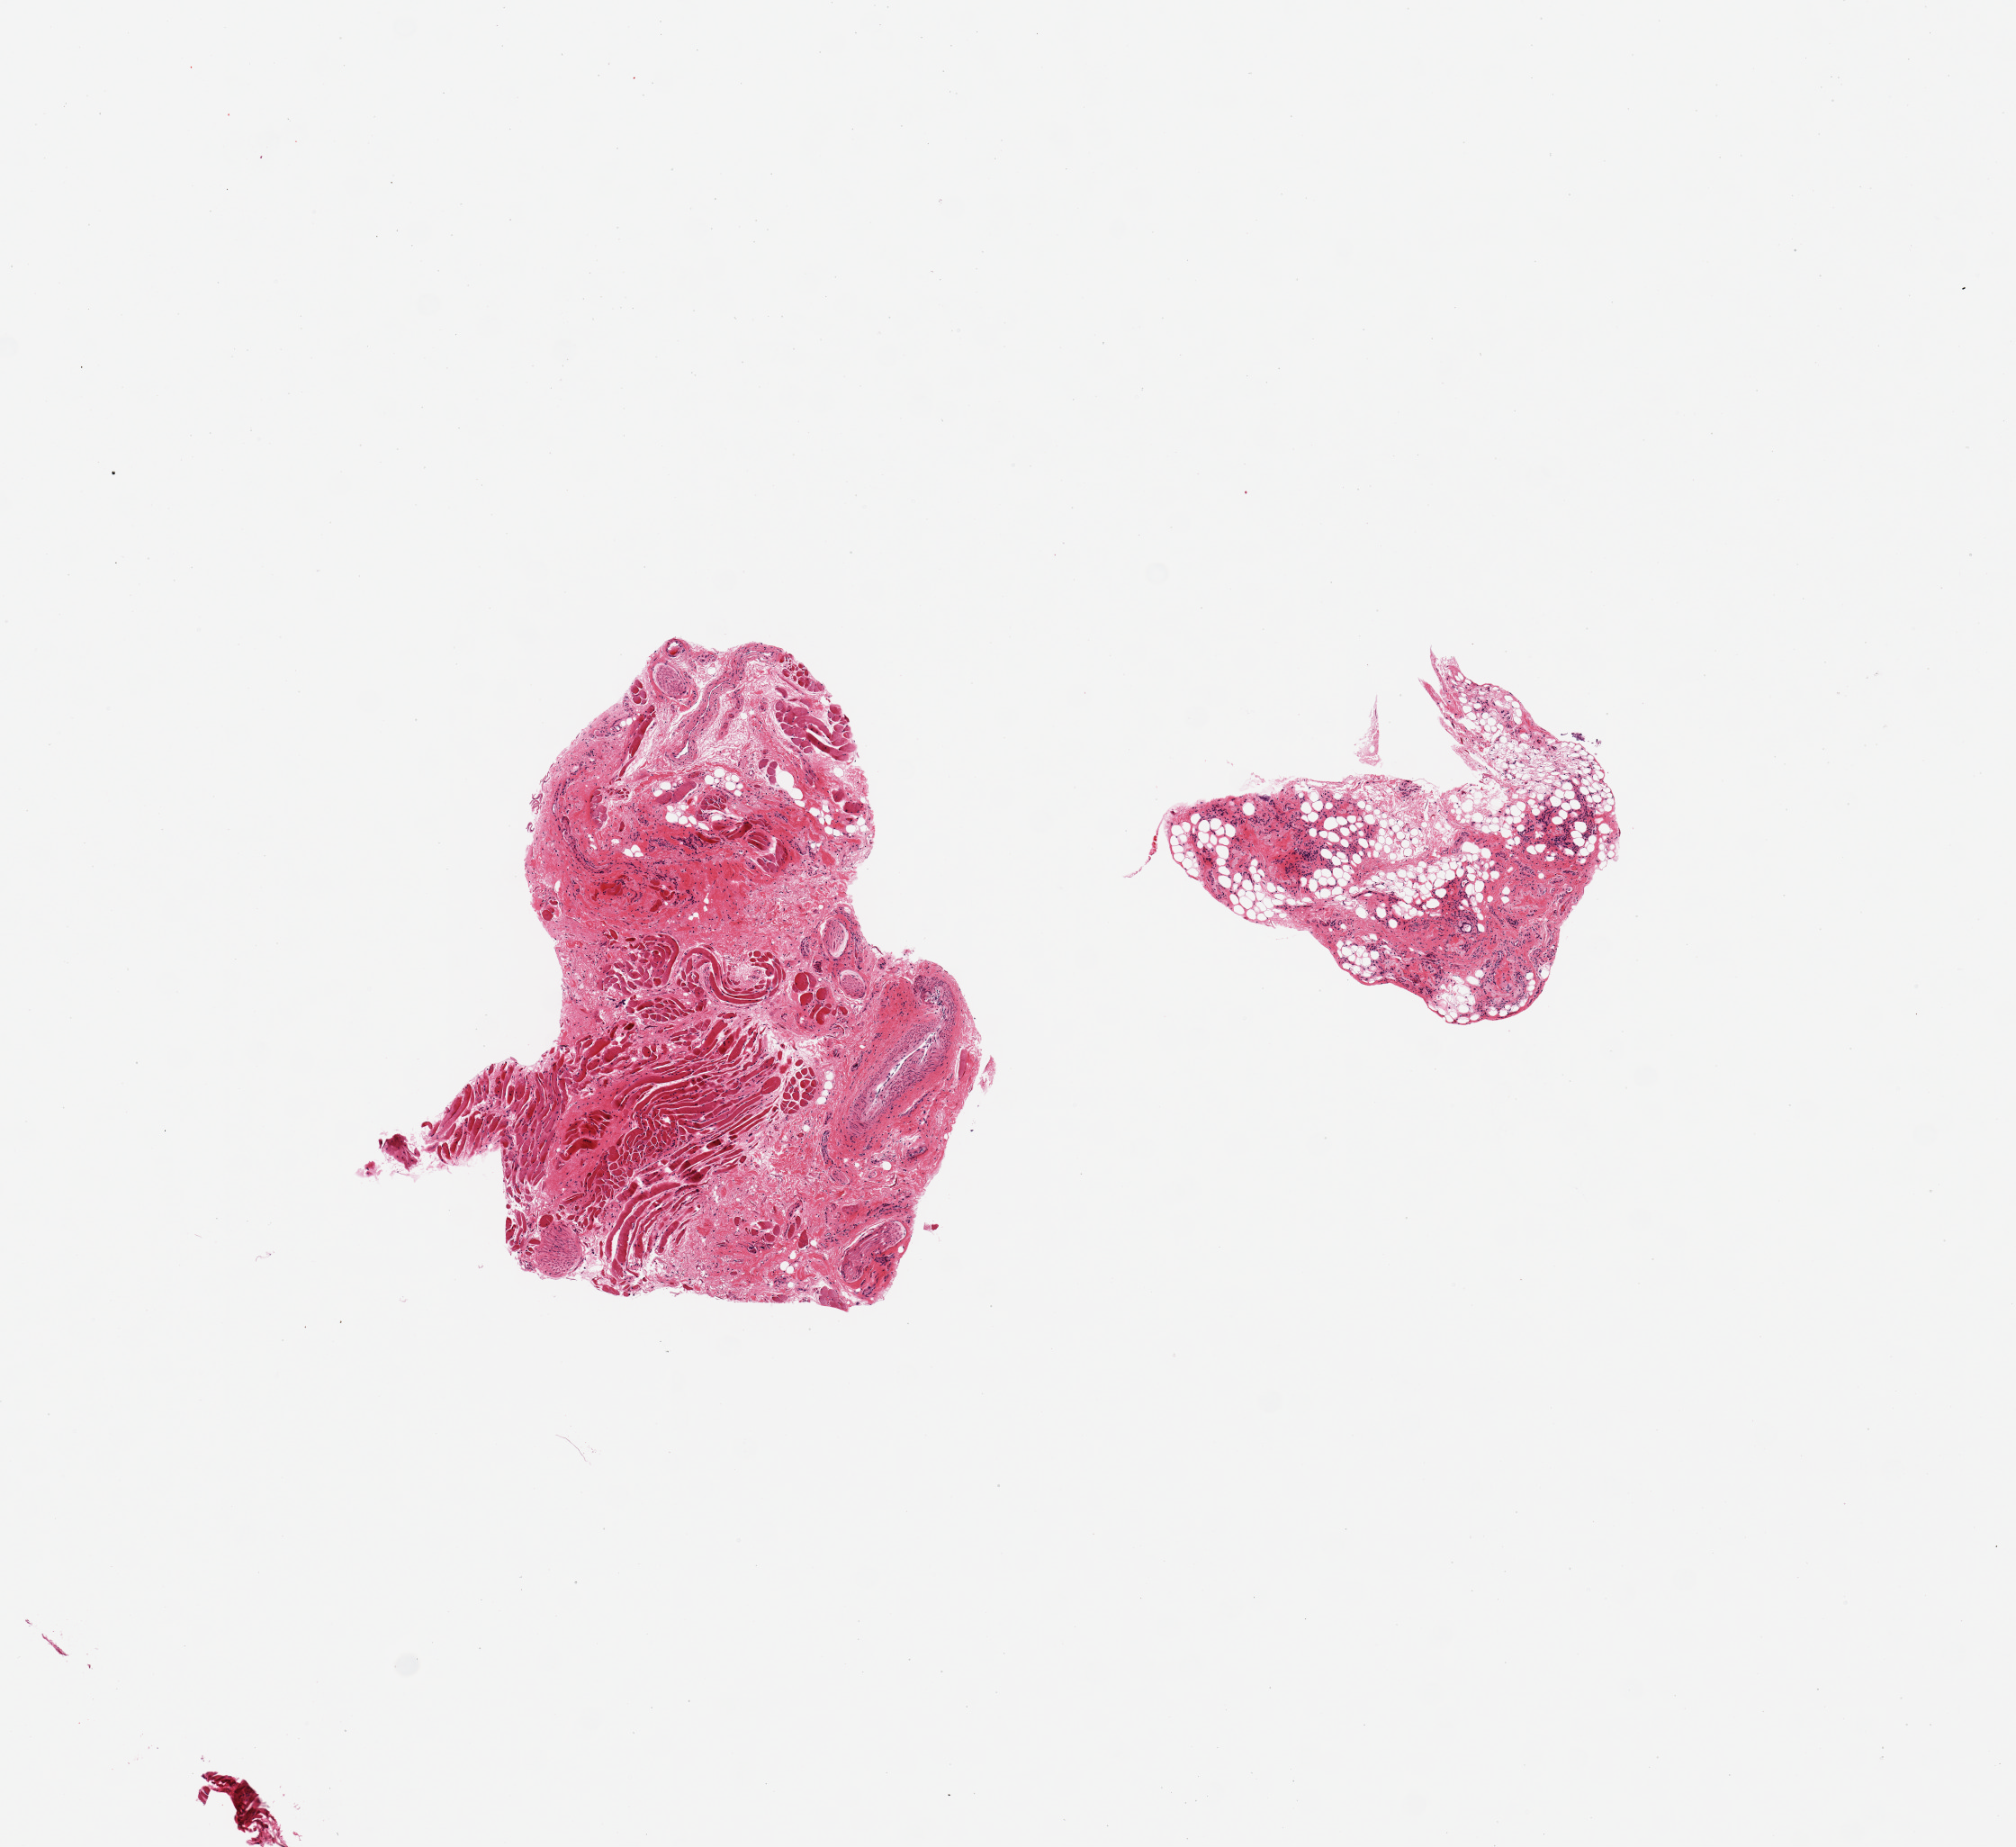
Digitized haematoxylin and eosin-stained section, brightfield — whole scanned area (about 8.9 x 8.1 mm) shown as a low-resolution overview; PAXgene-fixed, paraffin-embedded tissue; target tissue: minor salivary gland; tissue donor sample. Donor sex: male.
Reviewer comment on this tissue sample: 2 pieces, stroma, fat, skeletal muscle, and nerve.